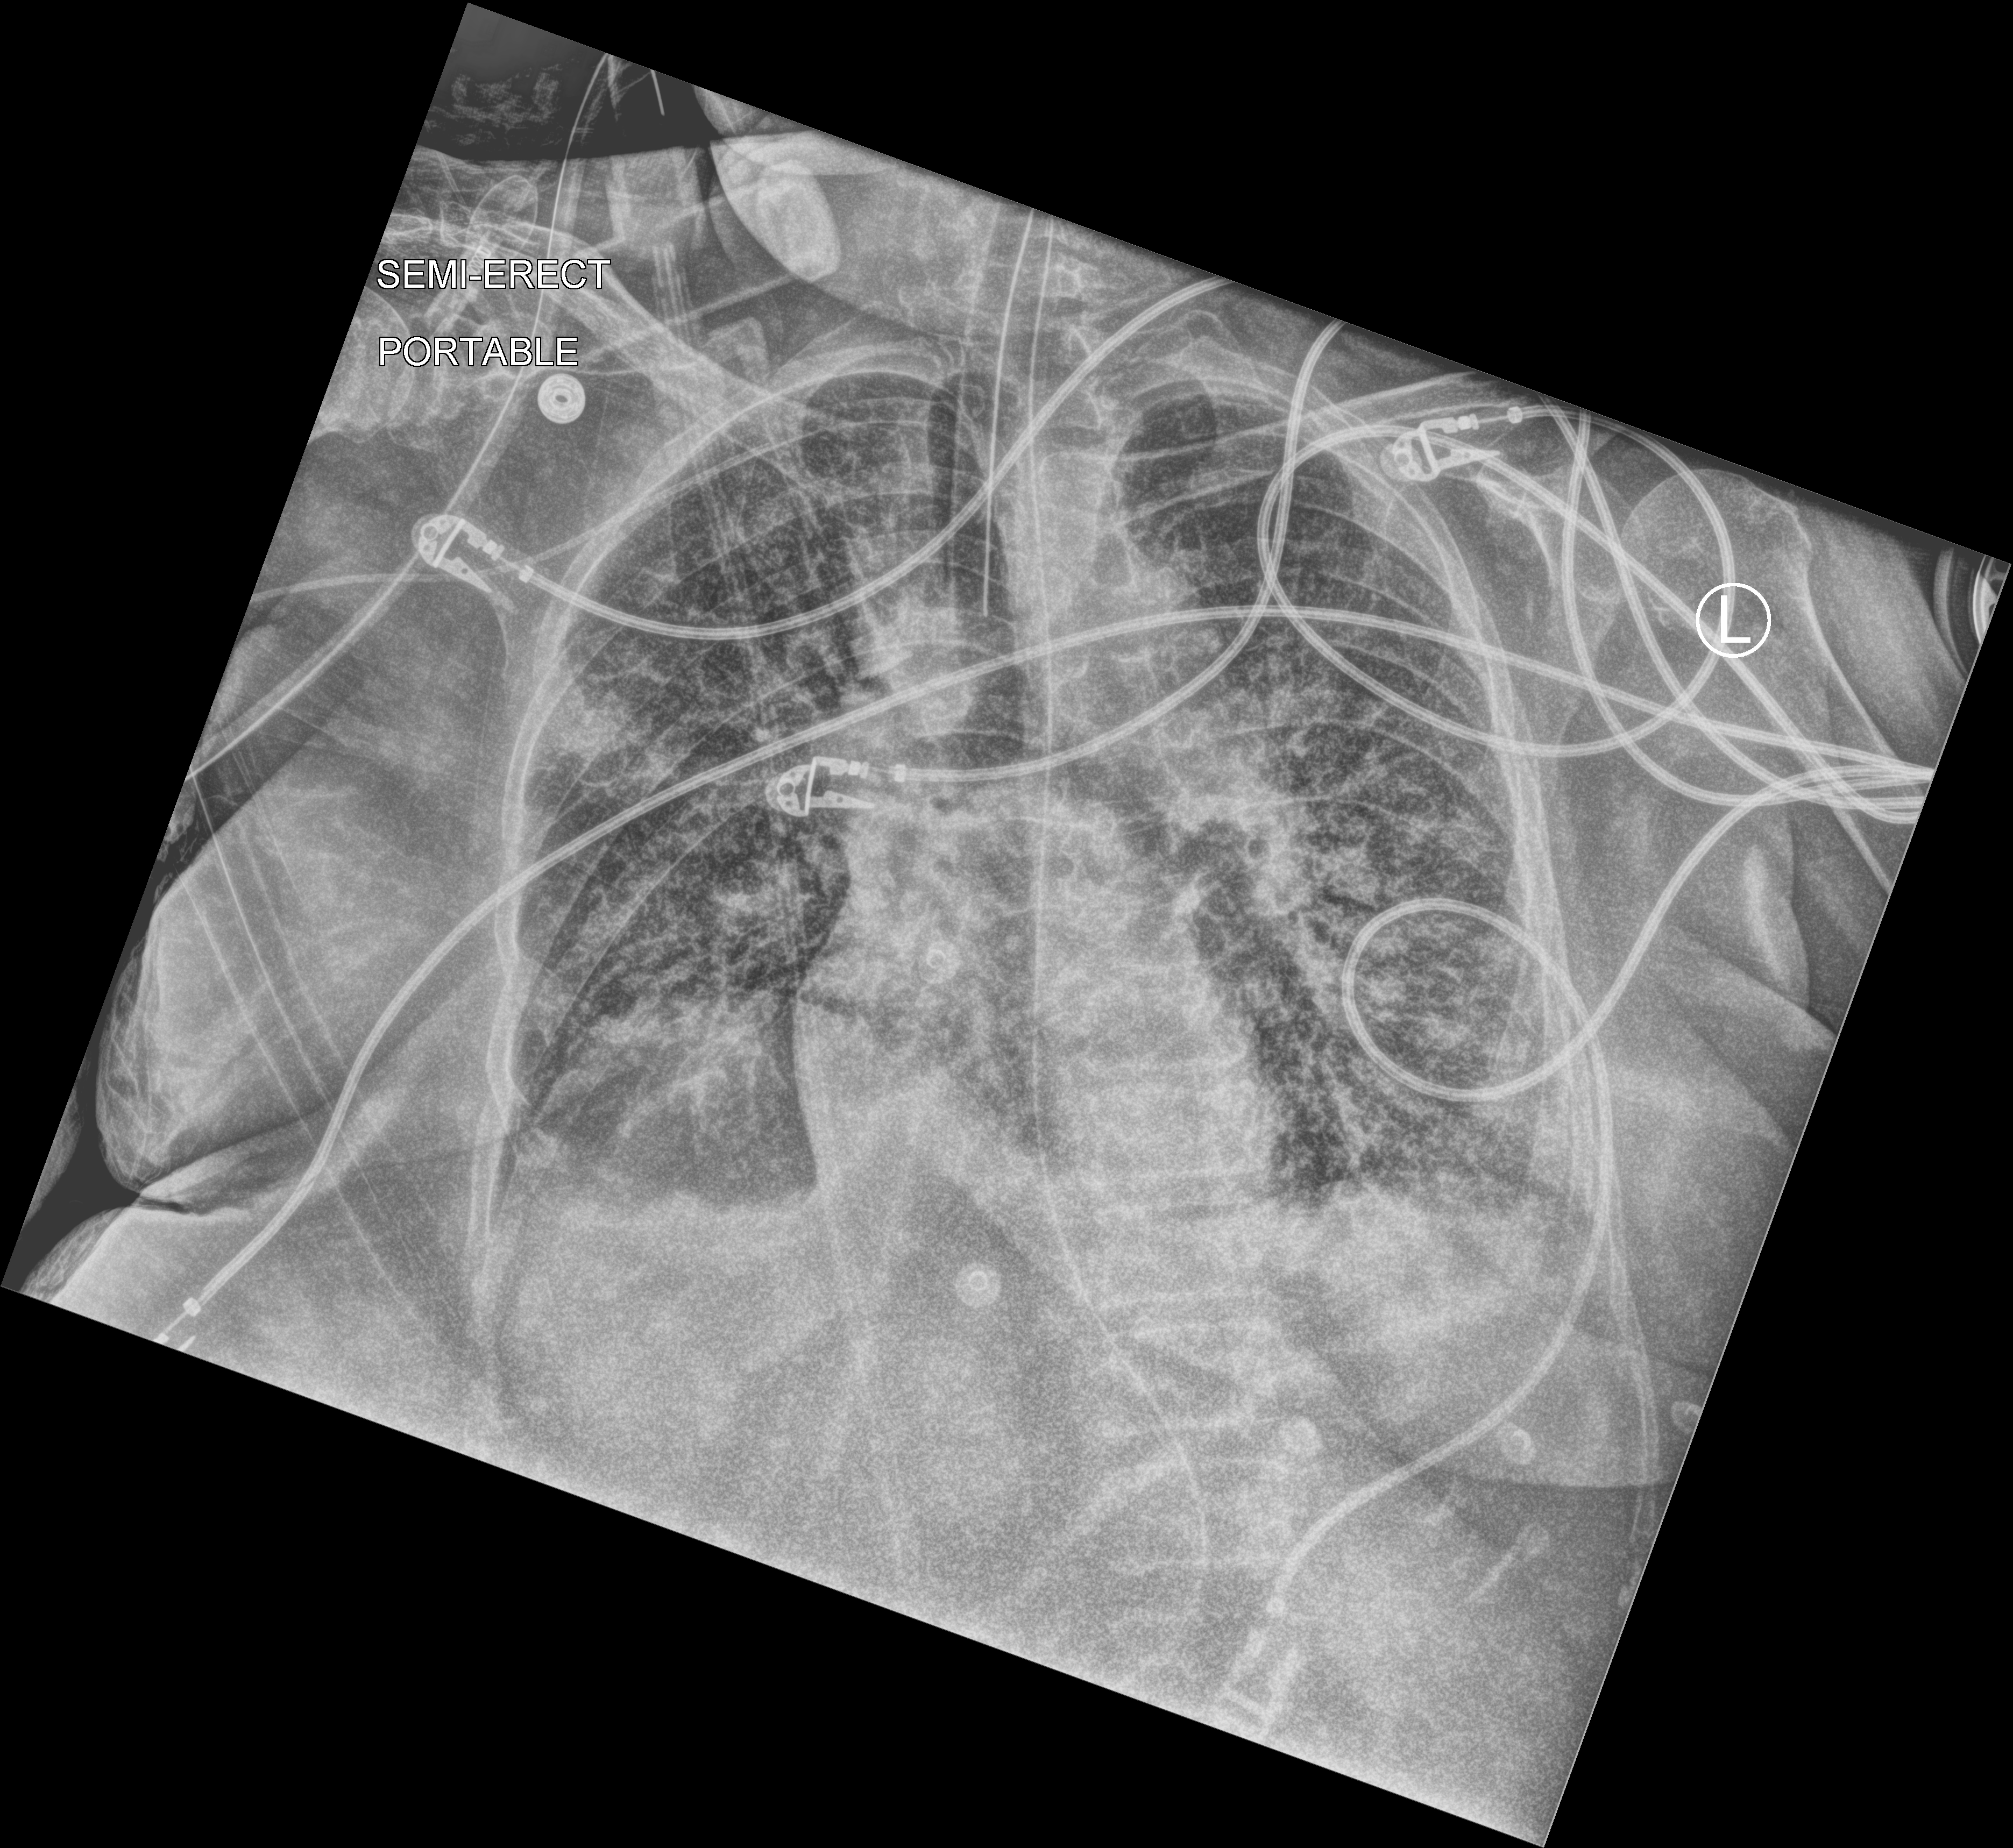
Bedside chest radiograph (computed radiography); anteroposterior (AP) projection. Female patient hospitalised with COVID-19, age 60–74 years.
From the hospital-stay record, not from the radiograph (when in the stay this image was taken is not recorded): mechanically ventilated during this hospital stay: yes.